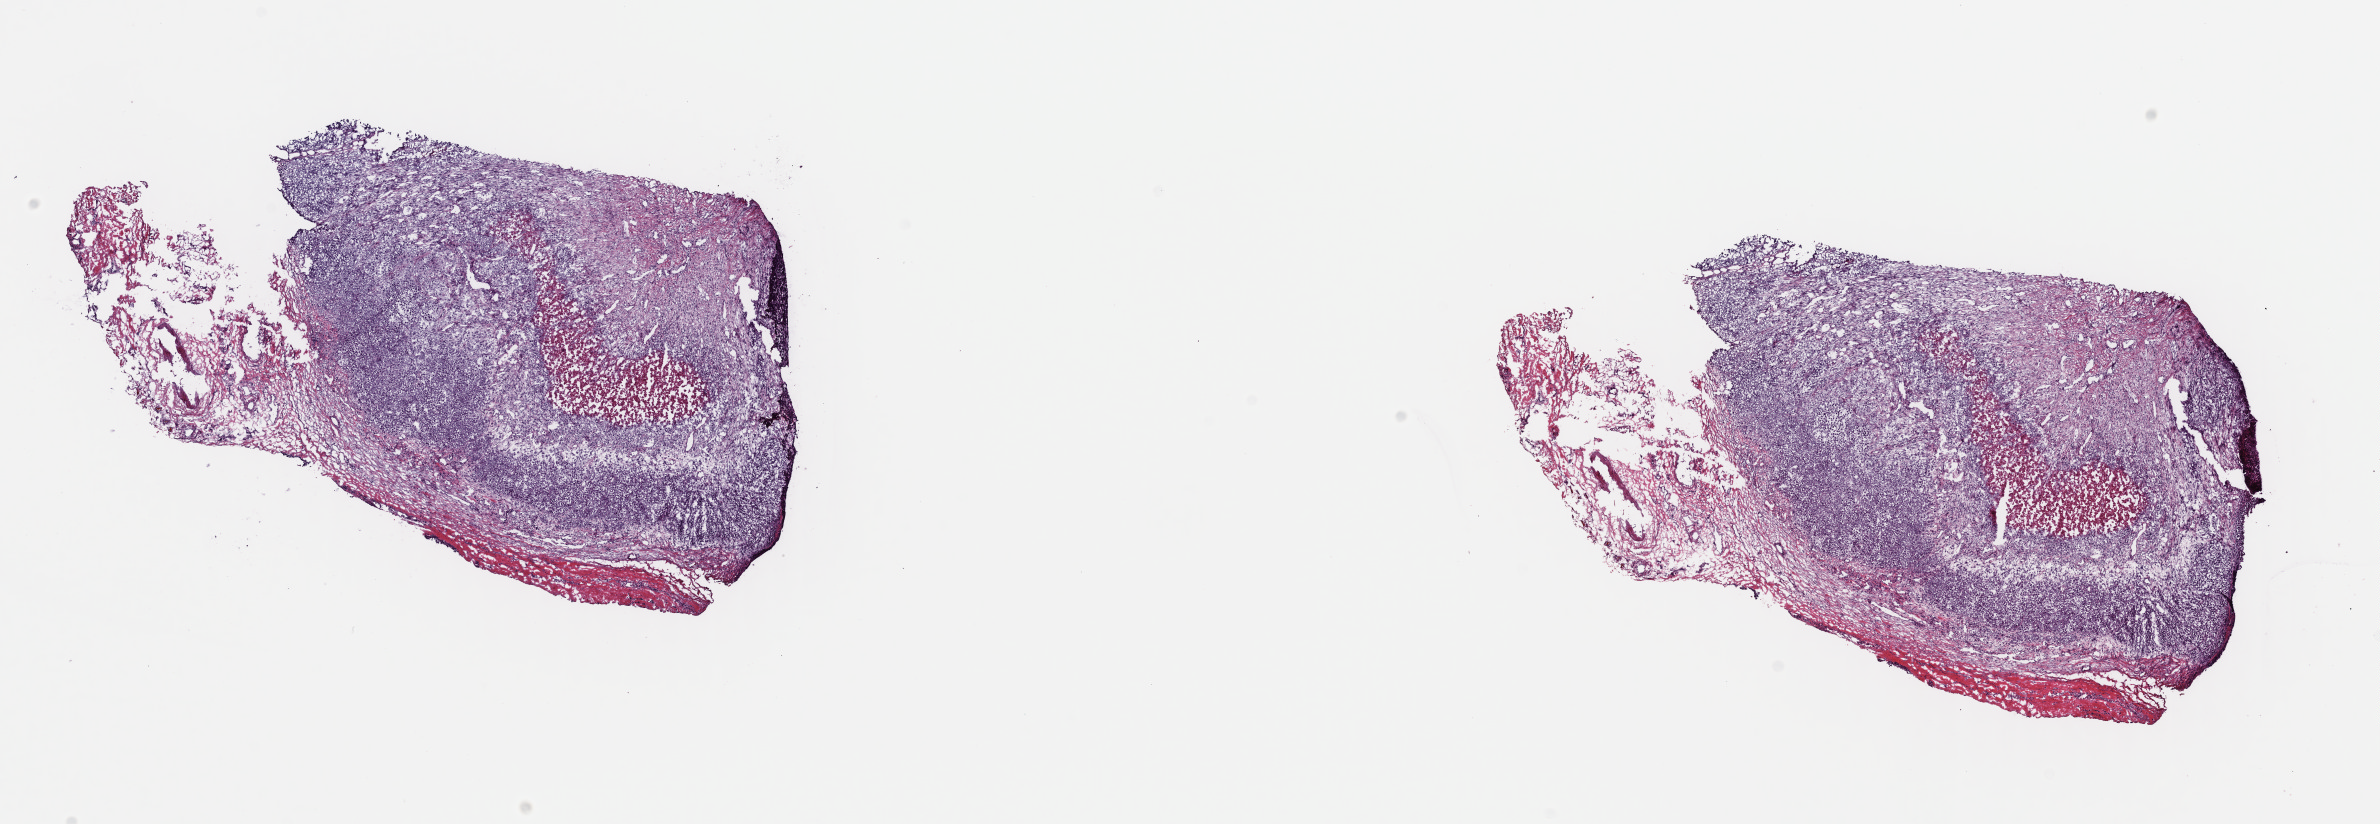
Whole-slide histology image, H&E — a low-resolution overview of the entire scanned area, about 18.8 x 6.5 mm; frozen section from the top of the tissue portion; metastatic tumour sample. Patient: male, age at initial diagnosis 19 years. Slide review estimates, as recorded: tumour cells 70%, tumour nuclei 70%, normal cells 0%, stromal cells 24%, necrosis 6%. Infiltration values recorded for this section: lymphocyte infiltration 1%, monocyte infiltration 2%, neutrophil infiltration 1%.
* this section: metastatic tumour tissue
* patient diagnosis: Malignant melanoma, NOS